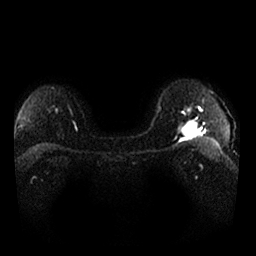
Breast MRI, one axial slice; slice 15 of 25 in the series (ordered by position); diffusion-weighted series; image 2 of 4 stored at this slice position (different b-values; order by instance number); 1.5 T; 256 × 256 image matrix, field of view 340 × 340 mm. Female patient.
Outlined on this slice (outlined manually by an expert reader):
- tumour on diffusion-weighted imaging: bounding box (x1, y1, x2, y2) in pixels: (175, 120, 199, 138)